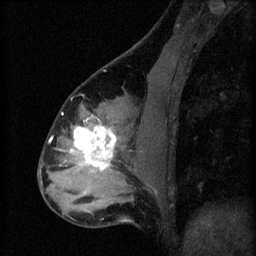
Breast MRI (dynamic contrast-enhanced), one sagittal slice. Position 25 of 60 along the scan axis. 3 images stored at this slice position (order not interpretable as contrast timing). 1.5 T. TE 4.2 ms, TR 8.2 ms. 2.3 mm slice thickness. 256 × 256 image matrix, field of view 180 × 180 mm. Female patient, age 37 years.
Outlined on this slice (semi-automatic segmentation, software-assisted and operator-edited):
- analysis volume of interest (the breast-tissue region the enhancement analysis was run in; not a lesion): bounding box (x1, y1, x2, y2) in pixels: (67, 120, 122, 179)
- tumour enhancement mask (voxels above the 70 % enhancement threshold inside the analysis volume of interest): (70, 120, 116, 171)